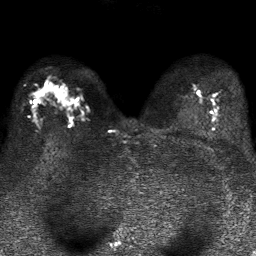
Breast MRI, one axial slice. Slice 25 of 37 in the series (ordered by position). Diffusion-weighted series; image 2 of 4 stored at this slice position (different b-values; order by instance number). 1.5 T. 5 mm slice thickness. 256 × 256 image matrix, field of view 320 × 320 mm. Female patient.
Structures marked on this image (expert manual segmentation):
- tumour on diffusion-weighted imaging: bounding box <59,93,63,97> (left, top, right, bottom; pixels)